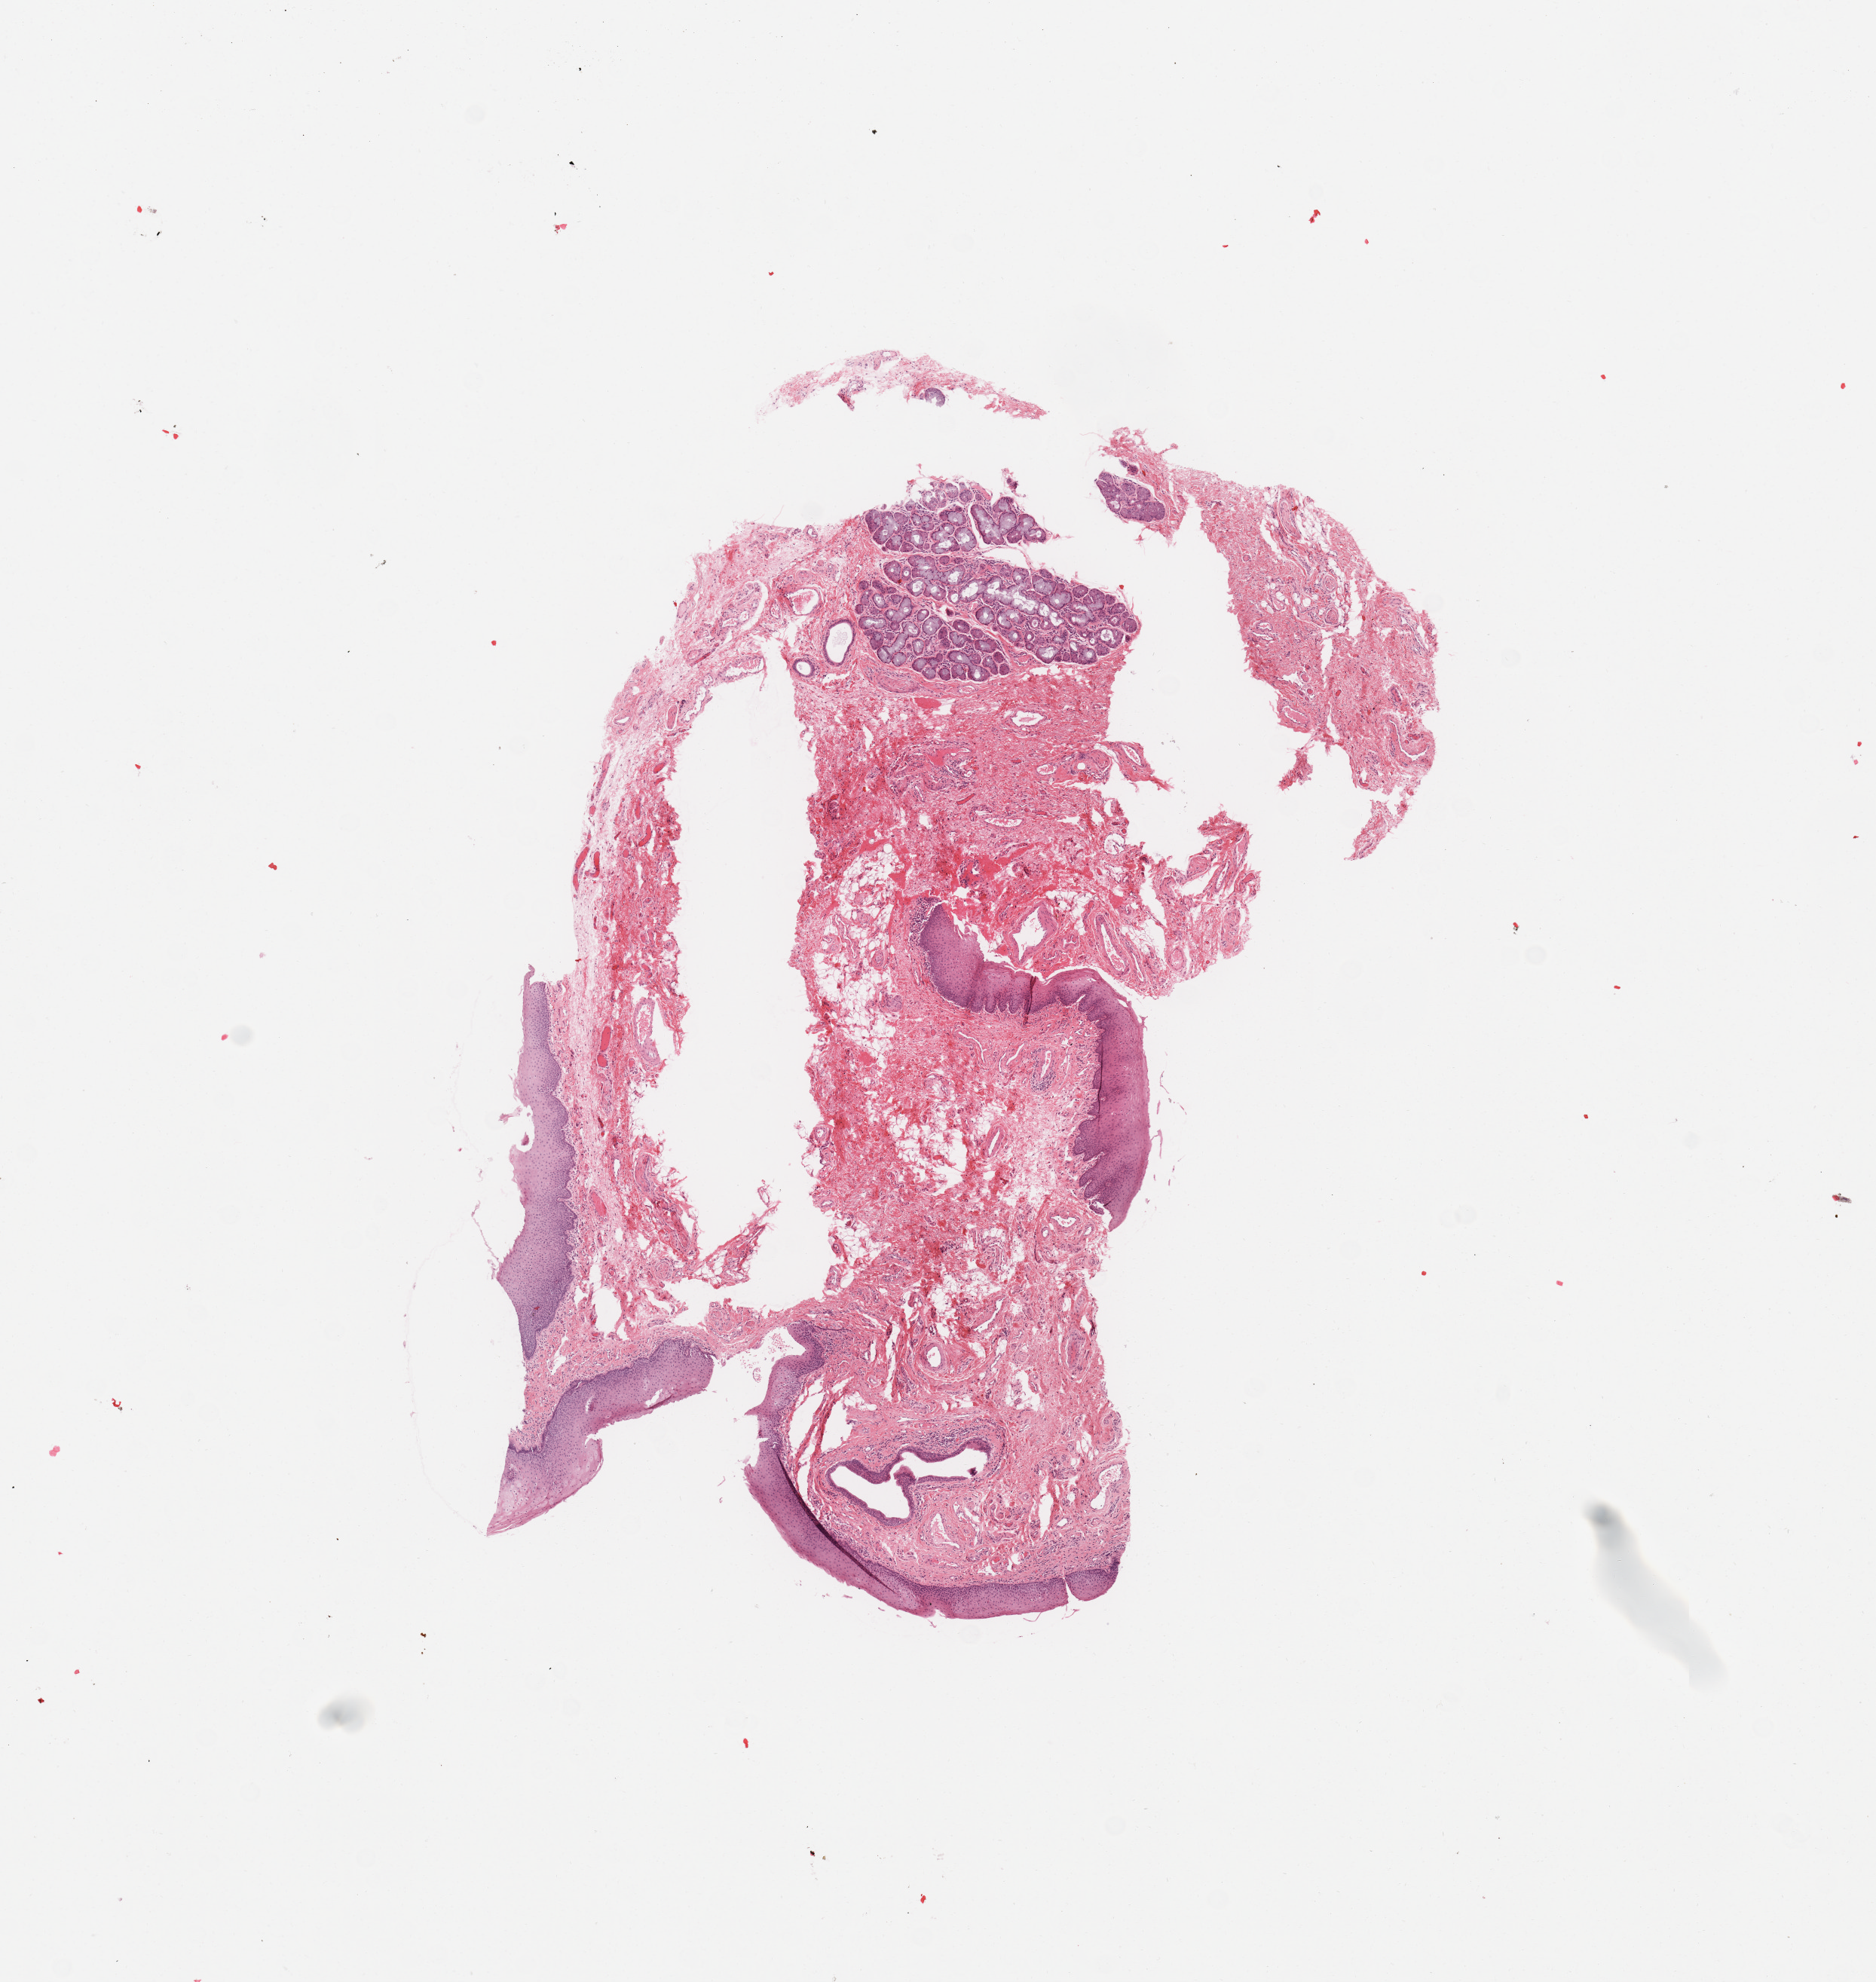
Digitized H&E-stained tissue section (whole slide), shown as a low-resolution overview of the whole scanned area (about 9.8 x 10.4 mm, acquisition: 20x scan), normal (non-tumour) tissue sample, sampled site: larynx. 52-year-old male patient.
• this section: normal (non-tumour) tissue from the same patient
• patient diagnosis: Squamous cell carcinoma, NOS